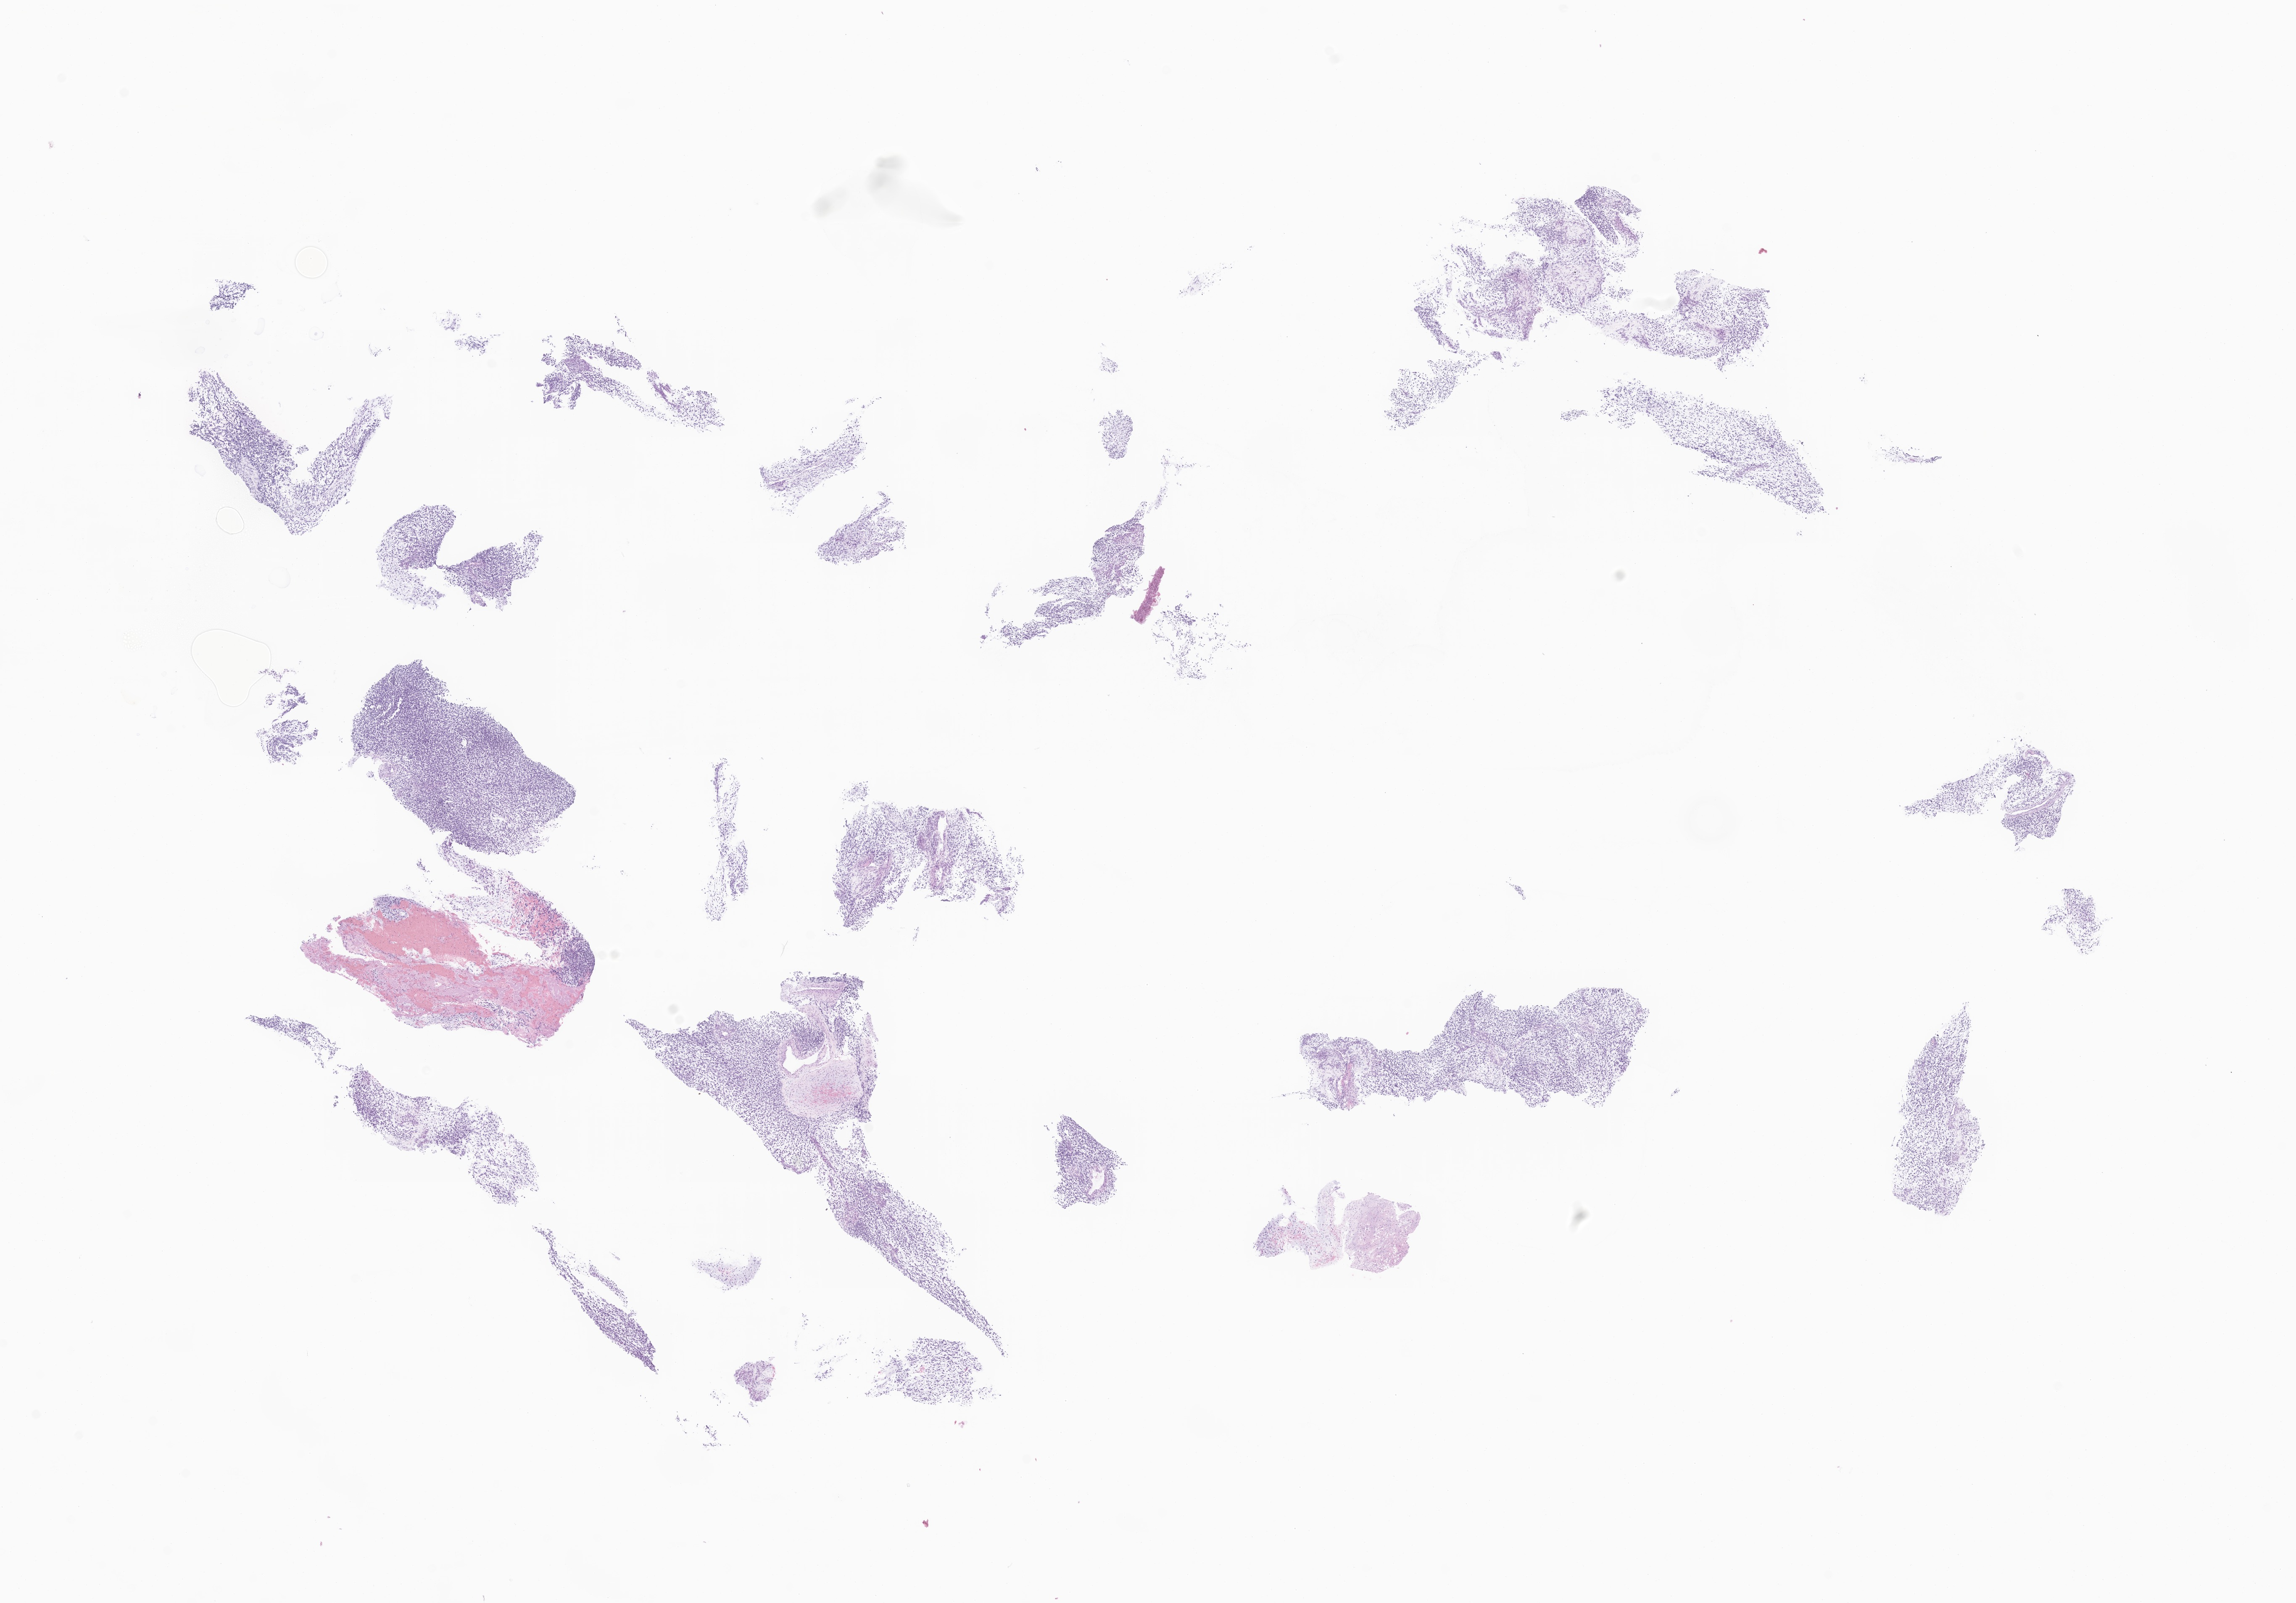
Whole-slide image, haematoxylin and eosin stain of tumor tissue from the soft tissue of pelvis, shown as a low-resolution overview of the whole scanned area (about 23.0 x 16.1 mm), formalin-fixed, paraffin-embedded (FFPE) tissue. Patient: male, age 523 days (about 1.4 years).
* recorded diagnosis: Embryonal rhabdomyosarcoma, NOS